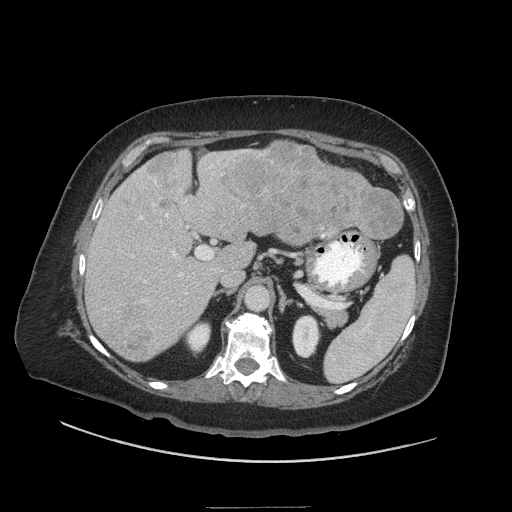
Contrast-enhanced abdominal CT (liver protocol), one axial slice. Slice 25 of 81 in the series (ordered by position). Reconstruction kernel STANDARD. Soft-tissue window (W 400 / L 40 HU). 2.5 mm slice thickness. 512 × 512 image matrix, field of view 440 × 440 mm. Case-level facts recorded for this patient, not image findings: diagnosis: hepatocellular carcinoma (patient treated with transarterial chemoembolisation; whether this scan precedes or follows treatment is not stated here); TNM stage (as recorded): Stage-II; Child-Pugh class: A; tumour differentiation: moderately differentiated; tumour nodularity: multinodular.
Structures marked on this image (semi-automatic segmentation, software-assisted and operator-edited):
- liver parenchyma outside the tumour (the mass and vessels are separate outlines, so this box may not span the whole liver): bounding box [x1, y1, x2, y2] px = [86, 140, 396, 361]
- mass: [117, 144, 402, 359]
- liver vessels: [104, 167, 329, 330]